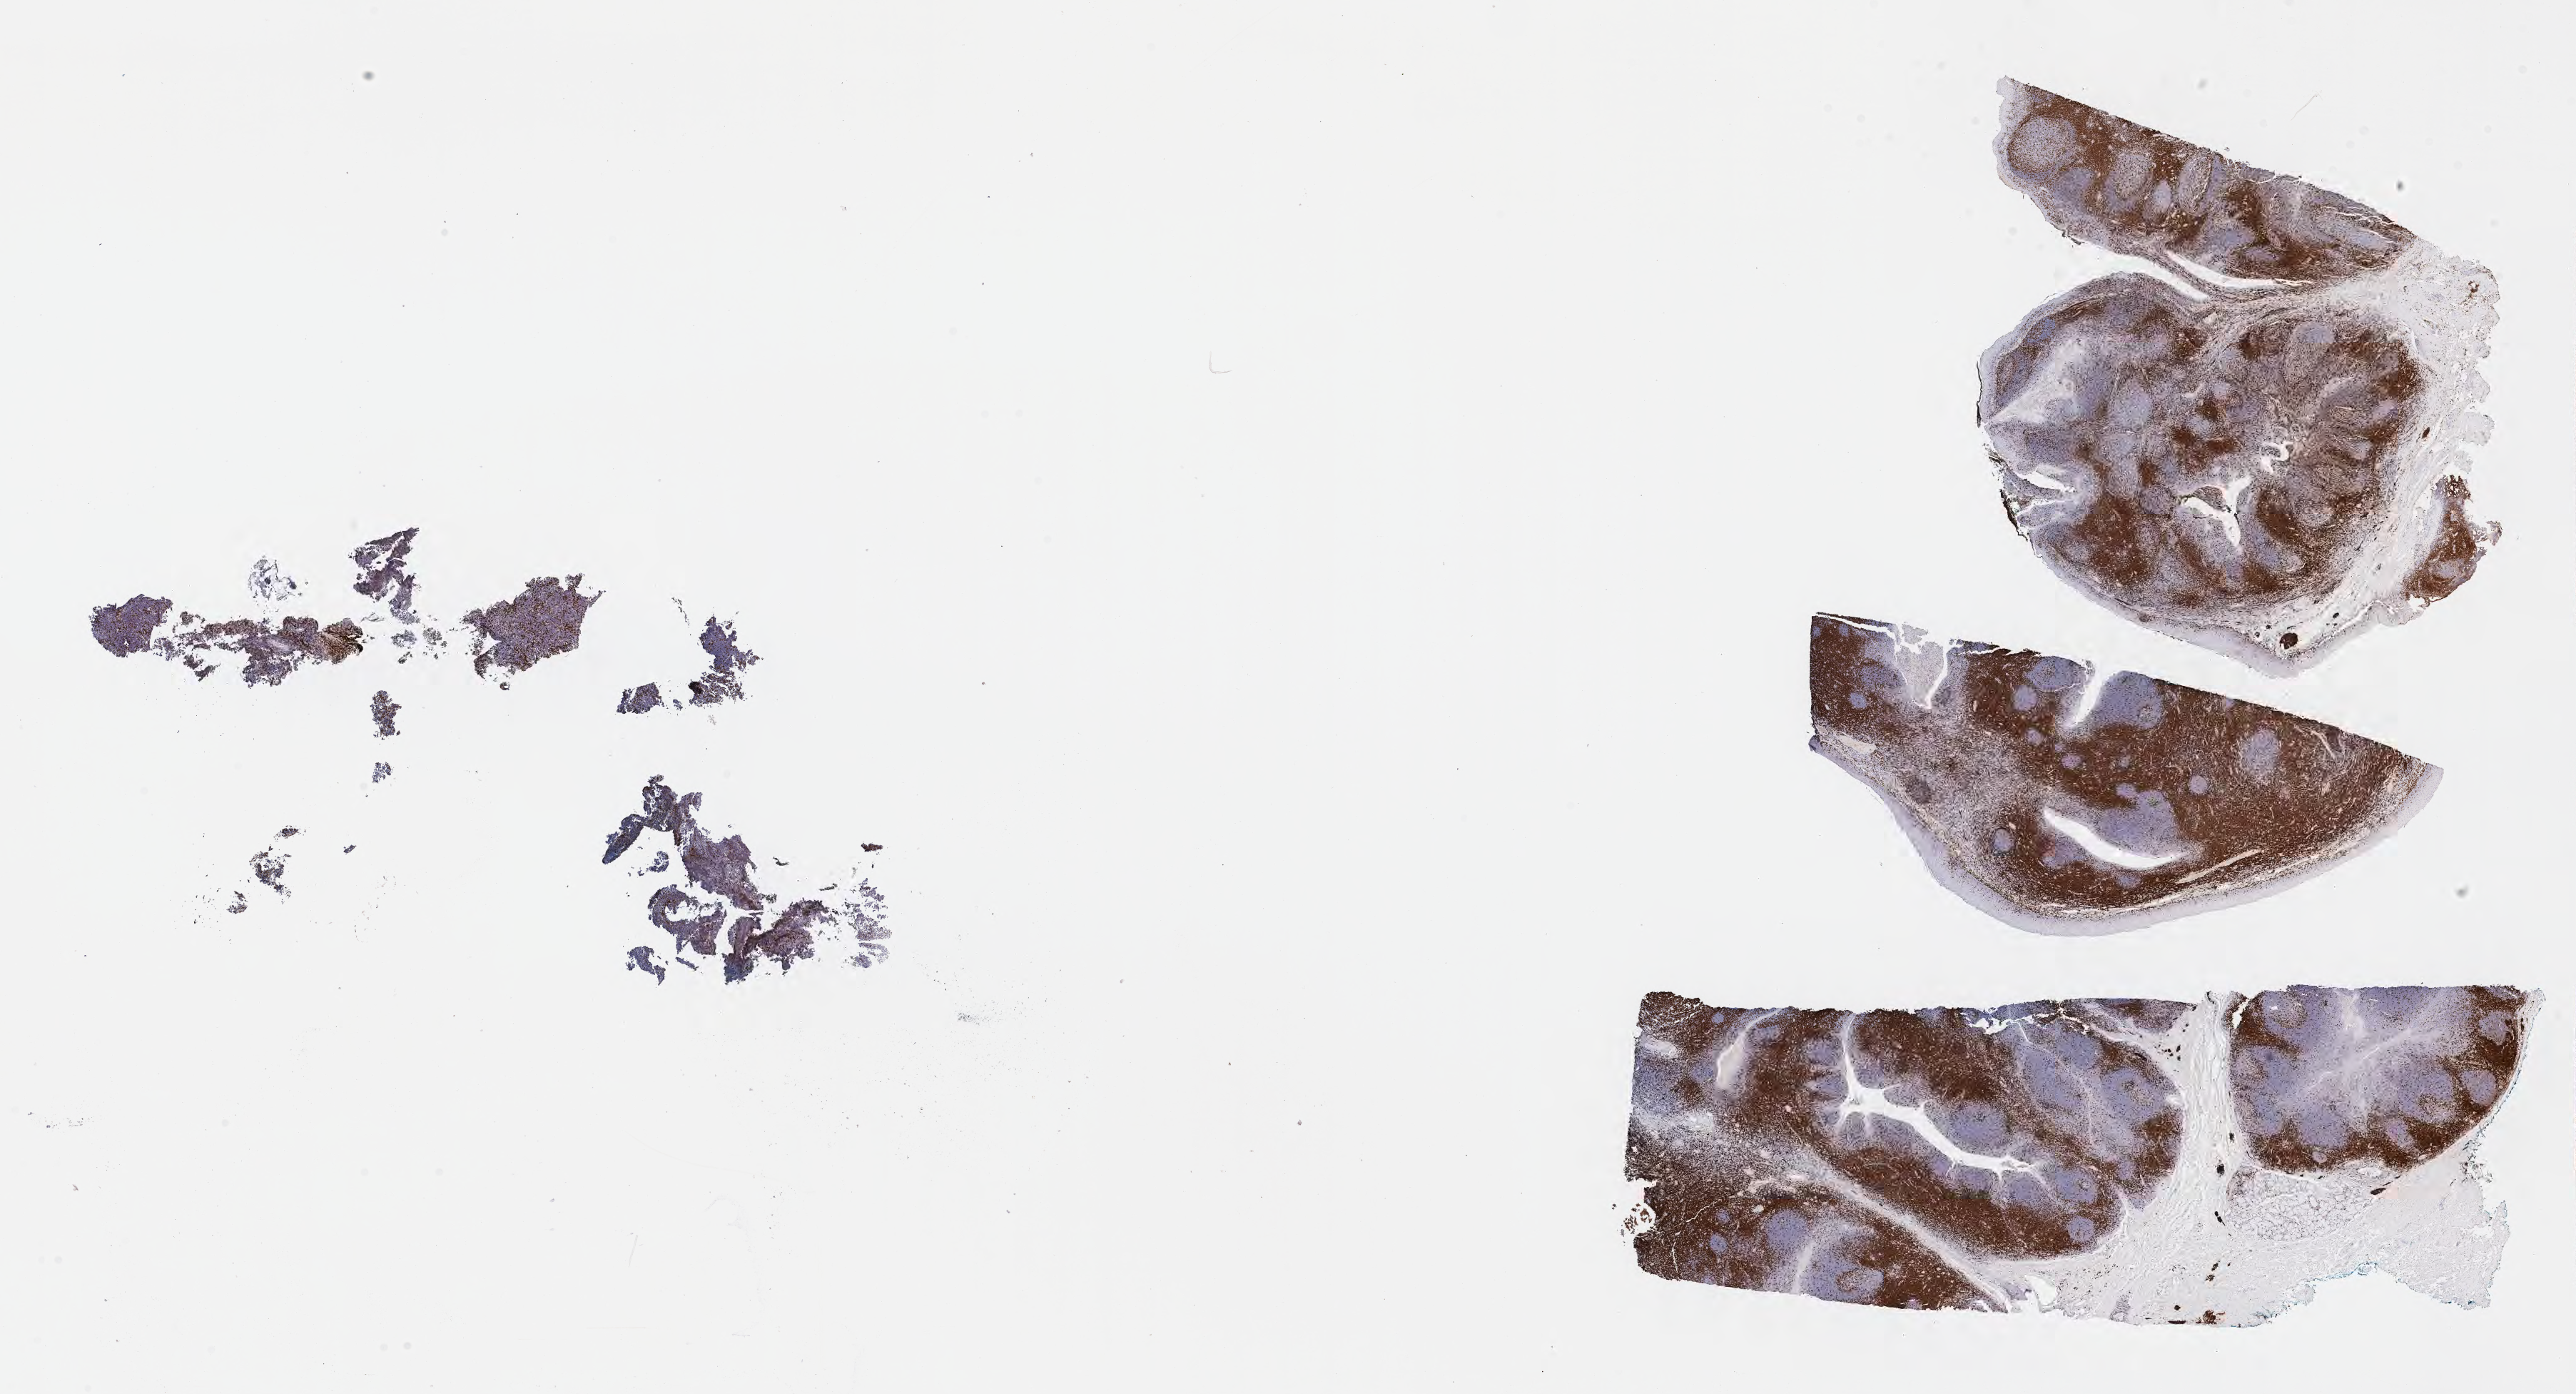
IHC for CD3, whole-slide image, shown as a low-resolution overview of the whole scanned area (about 29.2 x 15.8 mm); tumor tissue; anatomic site: cranium. Female, age 1 years at initial diagnosis.
Histologic diagnosis: Burkitt lymphoma, NOS.